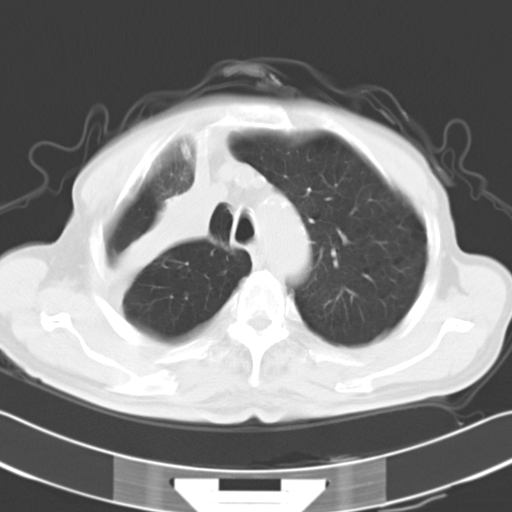
Chest CT, one axial slice; position 25 of 31 along the scan axis; reconstruction kernel B40f; 120 kVp; lung window (W 1500 / L -600 HU); 10 mm slice thickness; 512 × 512 image matrix. Male patient, age 73 years. Case-level facts recorded for this patient, not image findings: clinical TNM (as recorded): T2a N1 M0.
Outlined on this slice (bounding box drawn by a radiologist):
- lung tumour (recorded histology: squamous cell carcinoma): bounding box <114,146,223,277> (left, top, right, bottom; pixels)